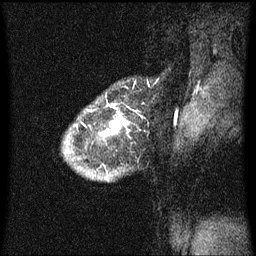
Breast MRI (dynamic contrast-enhanced), one sagittal slice. Position 54 of 60 along the scan axis. Dynamic contrast-enhanced series, image 2 of 3 at this slice position (ordered by acquisition). 1.5 T. TE 4.2 ms, TR 8.4 ms. 2 mm slice thickness. 256 × 256 image matrix. Patient: female, 34 years. From the clinical record (not read from this slice): setting: breast cancer imaged before/during neoadjuvant chemotherapy; receptor status: HR-positive, HER2-negative.
Structures marked on this image (semi-automatic segmentation, software-assisted and operator-edited):
- analysis volume of interest (the breast-tissue region the enhancement analysis was run in; not a lesion): bounding box [x1, y1, x2, y2] px = [62, 88, 147, 183]
- tumour enhancement mask (voxels above the 70 % enhancement threshold inside the analysis volume of interest): [108, 122, 127, 133]